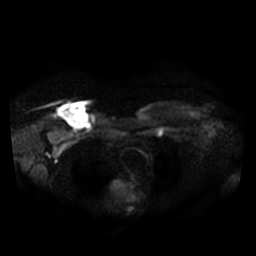
Breast MRI, one axial slice; position 31 of 36 along the scan axis; diffusion-weighted series; image 2 of 4 stored at this slice position (different b-values; order by instance number); 3 T; 5 mm slice thickness; 256 × 256 image matrix, field of view 340 × 340 mm. Female patient.
Annotated regions visible in this slice (manually delineated by an expert):
- tumour on diffusion-weighted imaging: bounding box (x1, y1, x2, y2) in pixels: (60, 105, 88, 128)